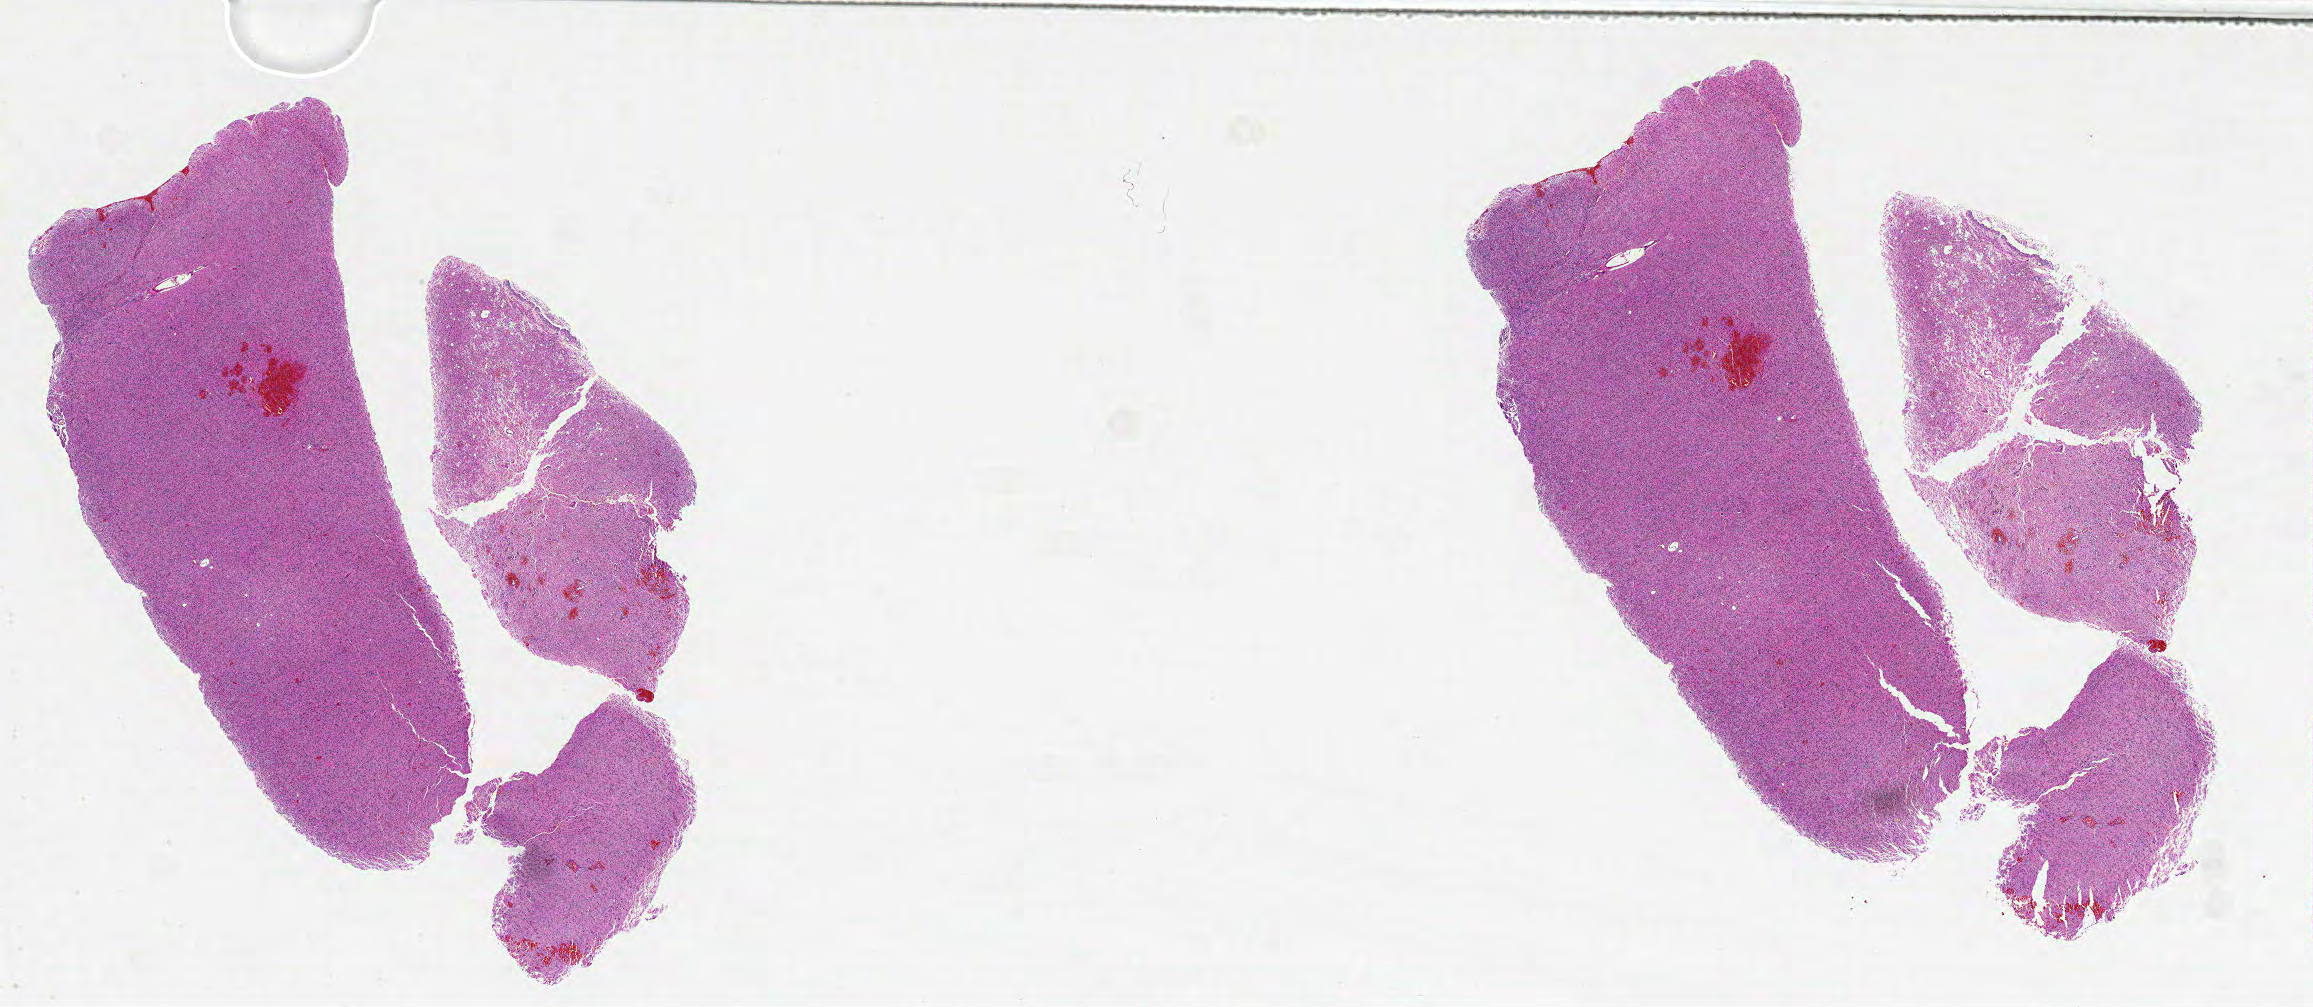
Hematoxylin and eosin (H&E) stained whole-slide image — shown as a low-resolution overview of the whole scanned area (about 37.0 x 16.1 mm, from a 20x scan); FFPE section; primary tumour sample from the brain. Patient: male, age at initial diagnosis 76 years.
Diagnosis: Glioblastoma.